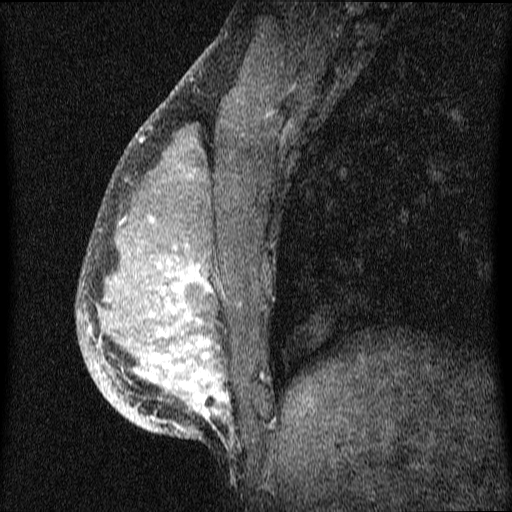
Breast MRI (dynamic contrast-enhanced), one sagittal slice; slice 25 of 64 in the series (ordered by position); dynamic contrast-enhanced series, image 2 of 4 at this slice position (ordered by acquisition); 1.5 T; TE 4.2 ms, TR 9.1 ms; 2 mm slice thickness; 512 × 512 image matrix, field of view 180 × 180 mm. Female patient, age 33 years.
Structures marked on this image (semi-automatic segmentation, software-assisted and operator-edited):
- analysis volume of interest (the breast-tissue region the enhancement analysis was run in; not a lesion): bounding box (x1, y1, x2, y2) in pixels: (77, 151, 334, 457)
- tumour enhancement mask (voxels above the 70 % enhancement threshold inside the analysis volume of interest): (90, 219, 230, 431)